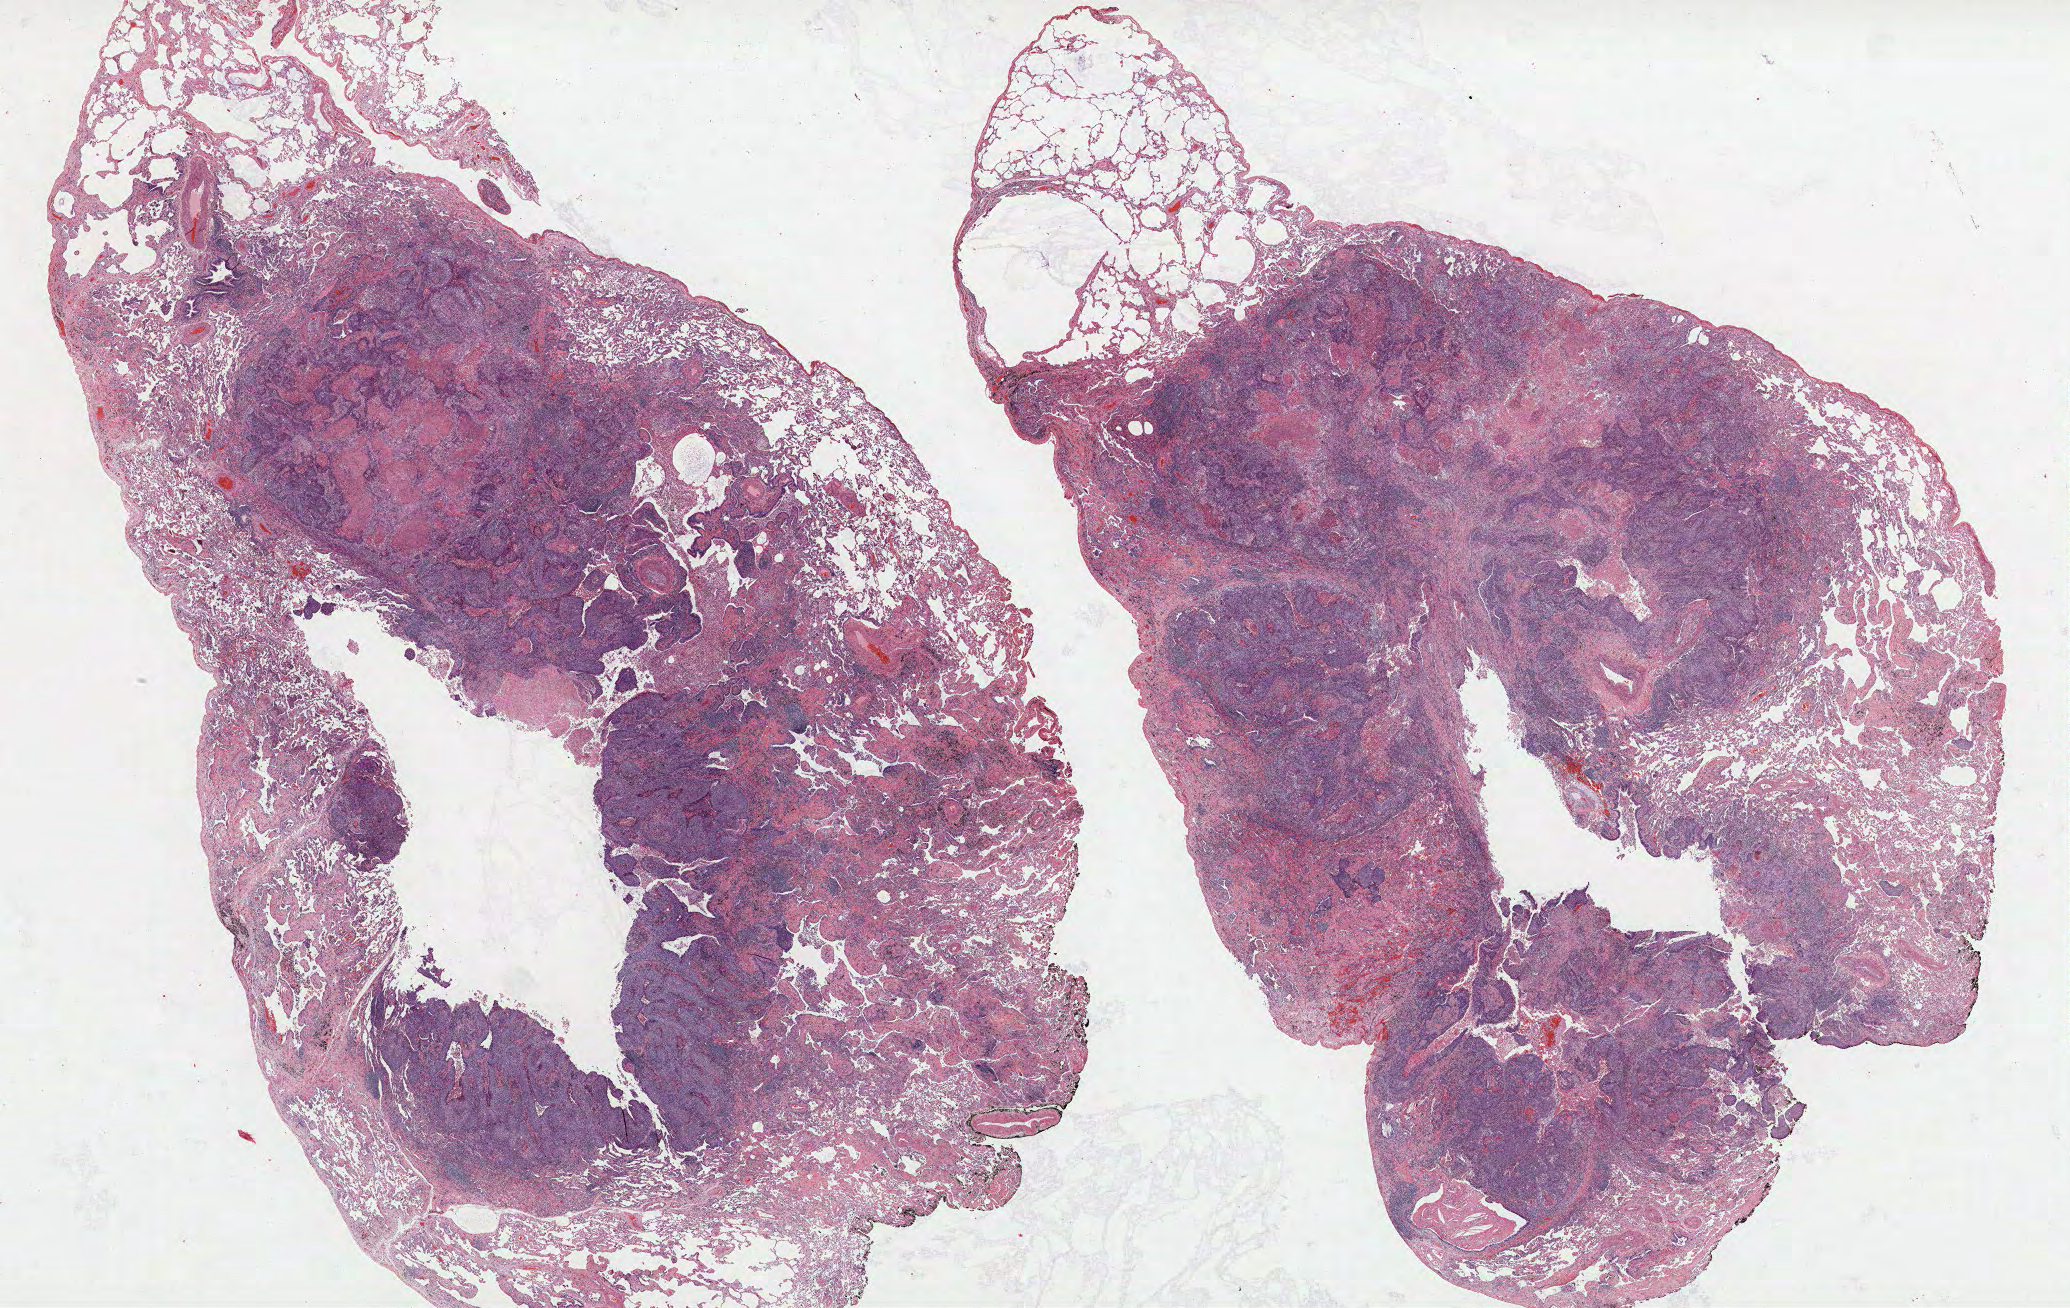
Whole-slide histology image, H&E-stained — a low-resolution overview of the entire scanned area, about 33.1 x 20.9 mm, formalin-fixed paraffin-embedded (FFPE) section, lung tissue. Male patient, aged 69 at enrolment. Current smoker at enrolment. Grade: moderately differentiated (G2).
Participant's lung-cancer diagnosis: Squamous cell carcinoma, NOS (ICD-O-3 8070/3). ICD-O-3 topography: lower lobe of lung (C34.3). Tumour size (pathology): 25 mm. Primary tumour location (clinical record): right lower lobe. Stage (AJCC 6th edition): IA.